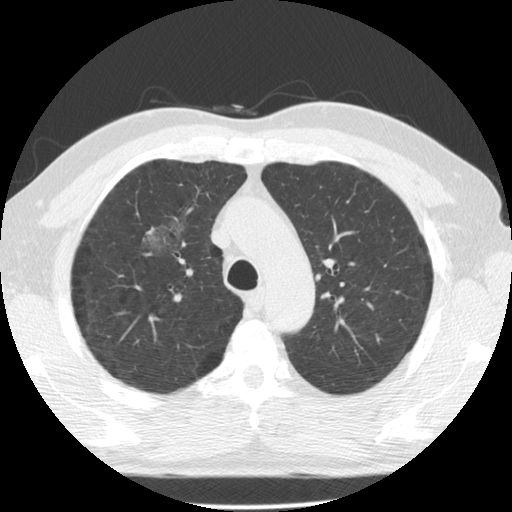
Low-dose screening chest CT, axial slice. Second annual screen. Lung window (W 1500 / L -600 HU). 2.5 mm slice thickness. Standard (soft-tissue) reconstruction kernel (STANDARD). 140 kVp. Slice 95 of 135 in the series. 512 × 512 image matrix, field of view 350 × 350 mm. Male participant, aged 60 years at enrolment. Former smoker at enrolment.
Lesion marked by an expert reader, box from (x=133, y=209) to (x=200, y=271) px. Screening reader's record for this exam (one nodule recorded; not confirmed to be the boxed lesion): non-calcified nodule or mass ≥4 mm, right upper lobe, poorly defined margins, mixed attenuation, pre-existing on the prior screen: yes; interval growth: yes. Participant outcome: lung cancer diagnosed 562 days after this screen (after the third annual screen) — papillary adenocarcinoma, NOS, right upper lobe, moderately differentiated (G2), stage IB (AJCC 6th edition), 32 mm at pathology.